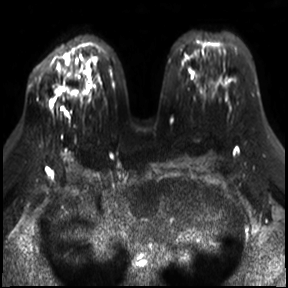
Breast MRI, one axial slice; position 18 of 30 along the scan axis; diffusion-weighted series; image 2 of 4 stored at this slice position (different b-values; order by instance number); 3 T; 288 × 288 image matrix, field of view 340 × 340 mm. Female patient.
Annotated regions visible in this slice (manually delineated by an expert):
- tumour on diffusion-weighted imaging: bounding box <50,101,52,106> (left, top, right, bottom; pixels)